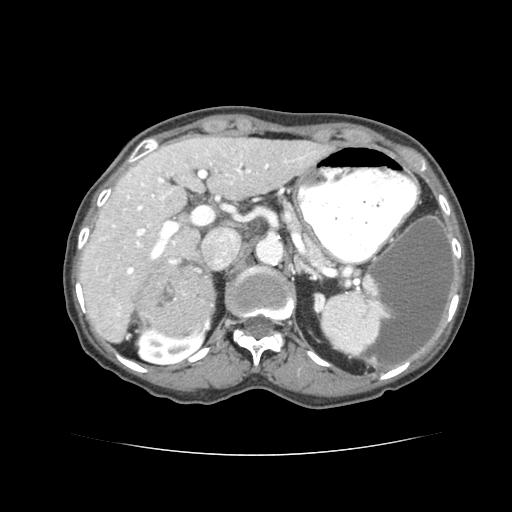
Contrast-enhanced abdominal CT (liver protocol), one axial slice; position 46 of 77 along the scan axis; reconstruction kernel STANDARD; 120 kVp; soft-tissue window (W 400 / L 40 HU); 2.5 mm slice thickness; 512 × 512 image matrix. From the clinical record (not read from this slice): diagnosis: hepatocellular carcinoma (patient treated with transarterial chemoembolisation; whether this scan precedes or follows treatment is not stated here); TNM stage (as recorded): Stage-I; Child-Pugh class: A; tumour differentiation: well differentiated.
Outlined on this slice (semi-automatically segmented with operator editing):
- liver parenchyma outside the tumour (the mass and vessels are separate outlines, so this box may not span the whole liver): bounding box (x1, y1, x2, y2) in pixels: (78, 134, 332, 338)
- mass: (136, 260, 215, 335)
- liver vessels: (88, 145, 287, 272)